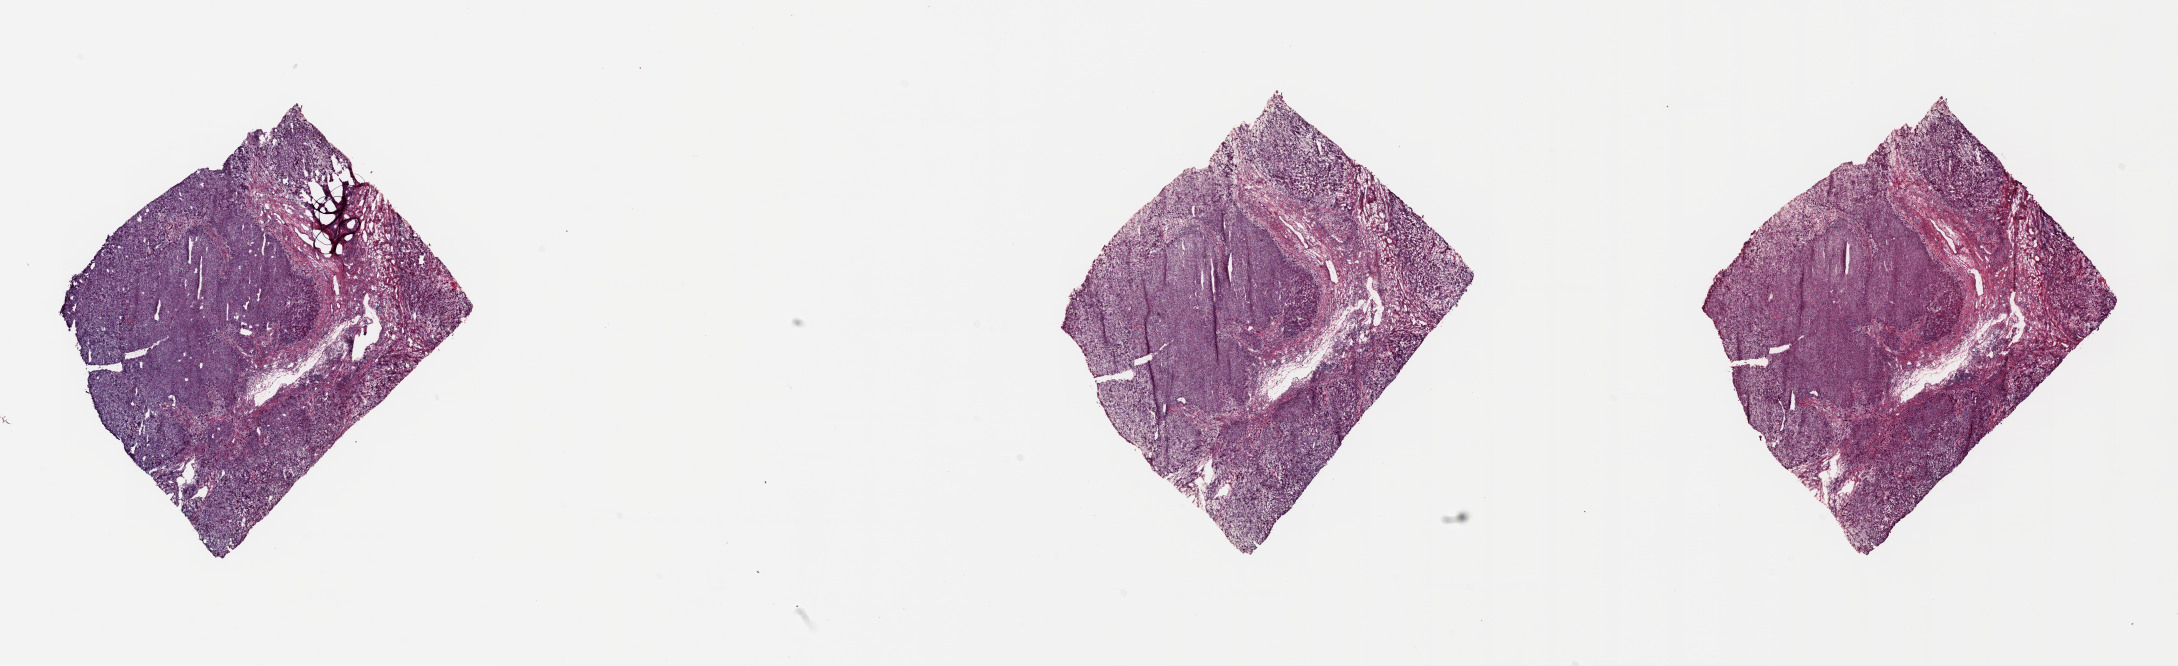
Digitized H&E tissue section (whole slide) — shown as a low-resolution overview of the whole scanned area (about 34.4 x 10.5 mm, acquisition: 20x scan), frozen section from the top of the tissue portion, liver, solid tissue normal (non-tumour tissue) sample. Female, age 85 years at initial diagnosis. Pathologist review of this section (percent, as recorded): tumour cells 0%, tumour nuclei 0%, normal cells 100%, stromal cells 0%, necrosis 0%. Inflammatory infiltration, as recorded: lymphocyte infiltration 10%, monocyte infiltration 0%, neutrophil infiltration 0%.
- this section: solid tissue normal sample (biorepository sample class)
- patient diagnosis: Hepatocellular carcinoma, NOS